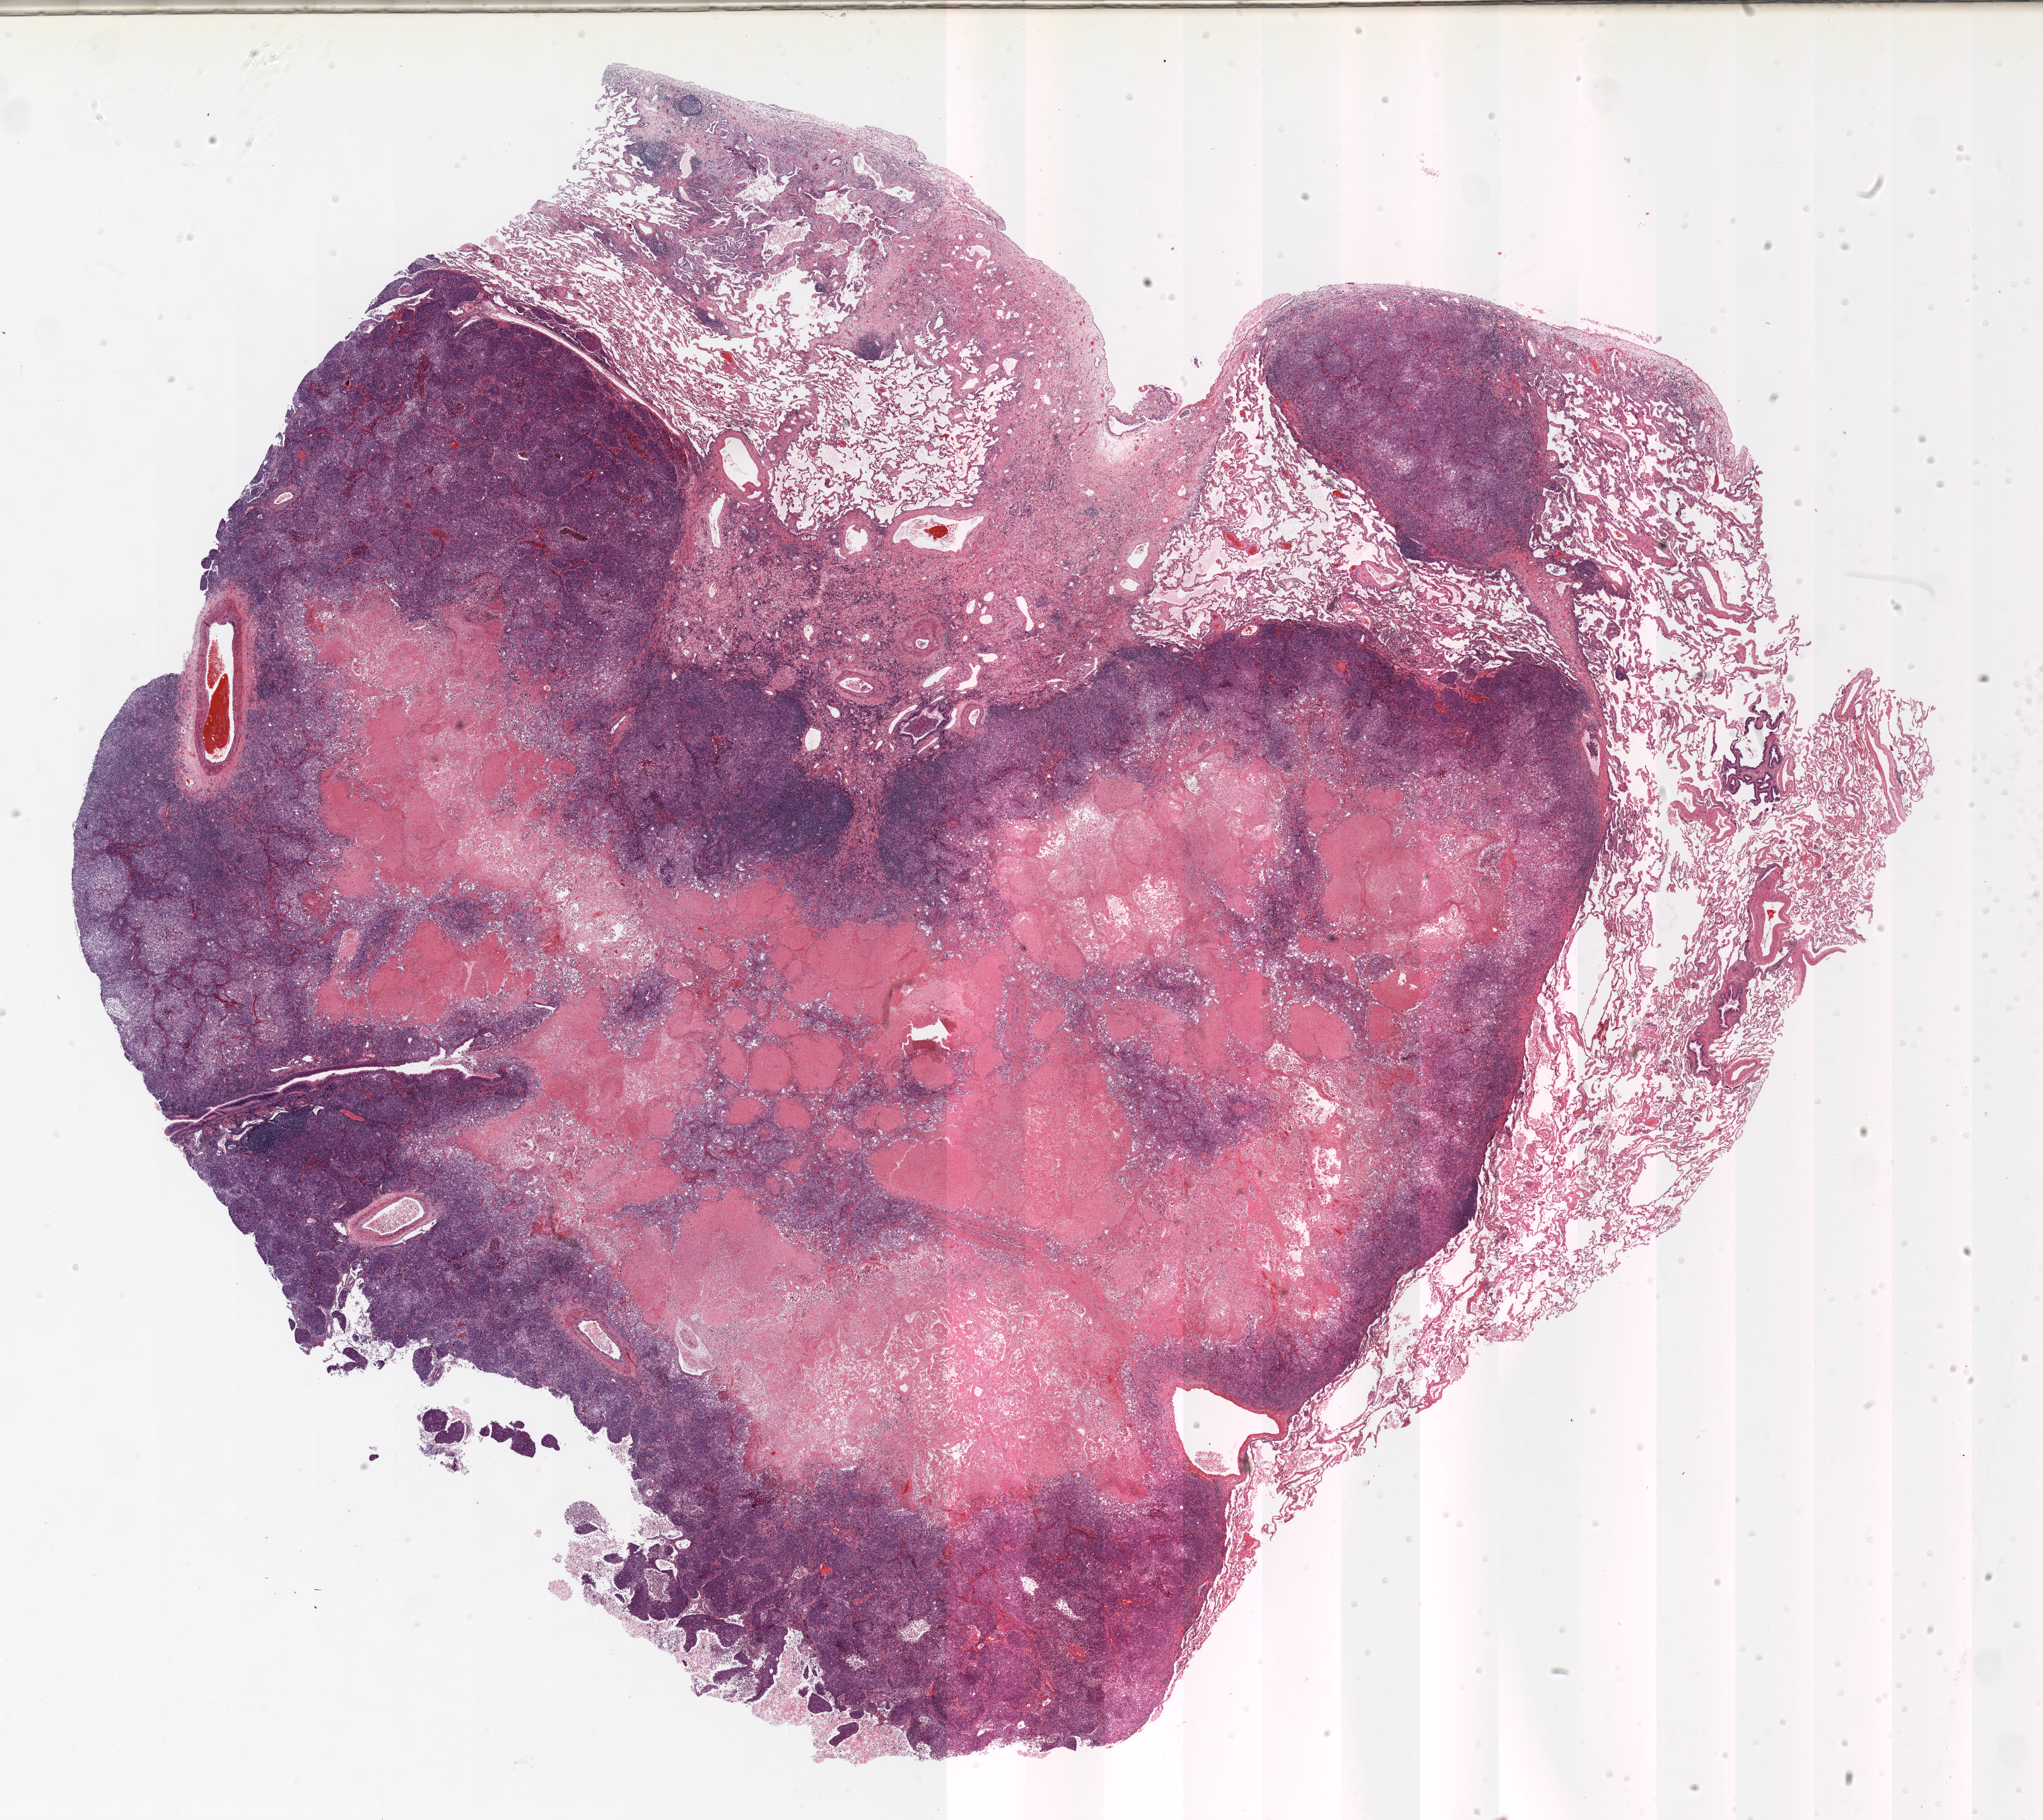
H&E-stained whole-slide image — whole scanned area (about 26.0 x 23.2 mm) shown as a low-resolution overview, formalin-fixed paraffin-embedded (FFPE) section, lung tissue. Female patient, aged 67 at enrolment. Grade: poorly differentiated (G3).
Stage (AJCC 6th edition): IA. Primary tumour location (clinical record): left upper lobe. Participant's lung-cancer diagnosis: Squamous cell carcinoma, NOS (ICD-O-3 8070/3). Tumour size (pathology): 25 mm.